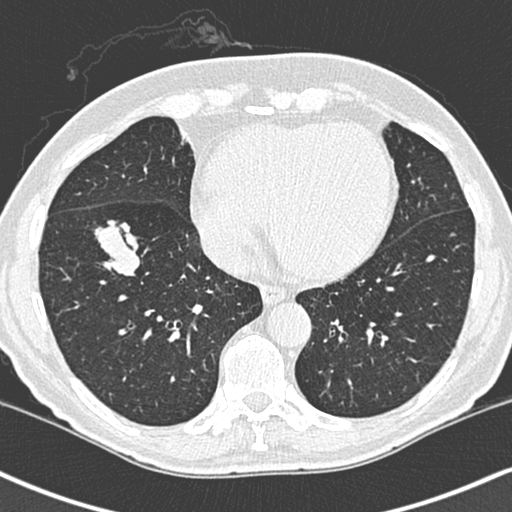
Low-dose screening chest CT, one axial slice; position 95 of 248 along the scan axis; lung window (W 1500 / L -600 HU); 512 × 512 image matrix, field of view 323 × 323 mm.
Structures marked on this image (outlined manually by an expert reader):
- lesion 1 (tumor, lower lobe of right lung): bounding box [x1, y1, x2, y2] px = [94, 182, 140, 238]